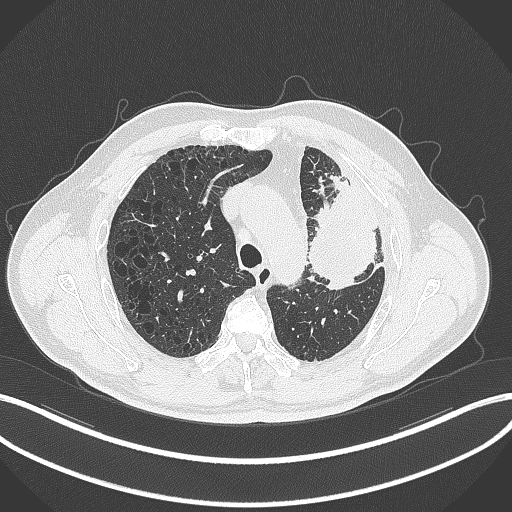
Chest CT, one axial slice; slice 232 of 297 in the series (ordered by position); reconstruction kernel B70f; lung window (W 1500 / L -600 HU); 1 mm slice thickness; 512 × 512 image matrix. Patient: male, 68 years. From the clinical record (not read from this slice): clinical TNM (as recorded): T3 N3 M1.
Structures marked on this image (rectangle marked by the reading radiologist):
- lung tumour (recorded histology: adenocarcinoma): box from (x=297, y=157) to (x=396, y=297) px